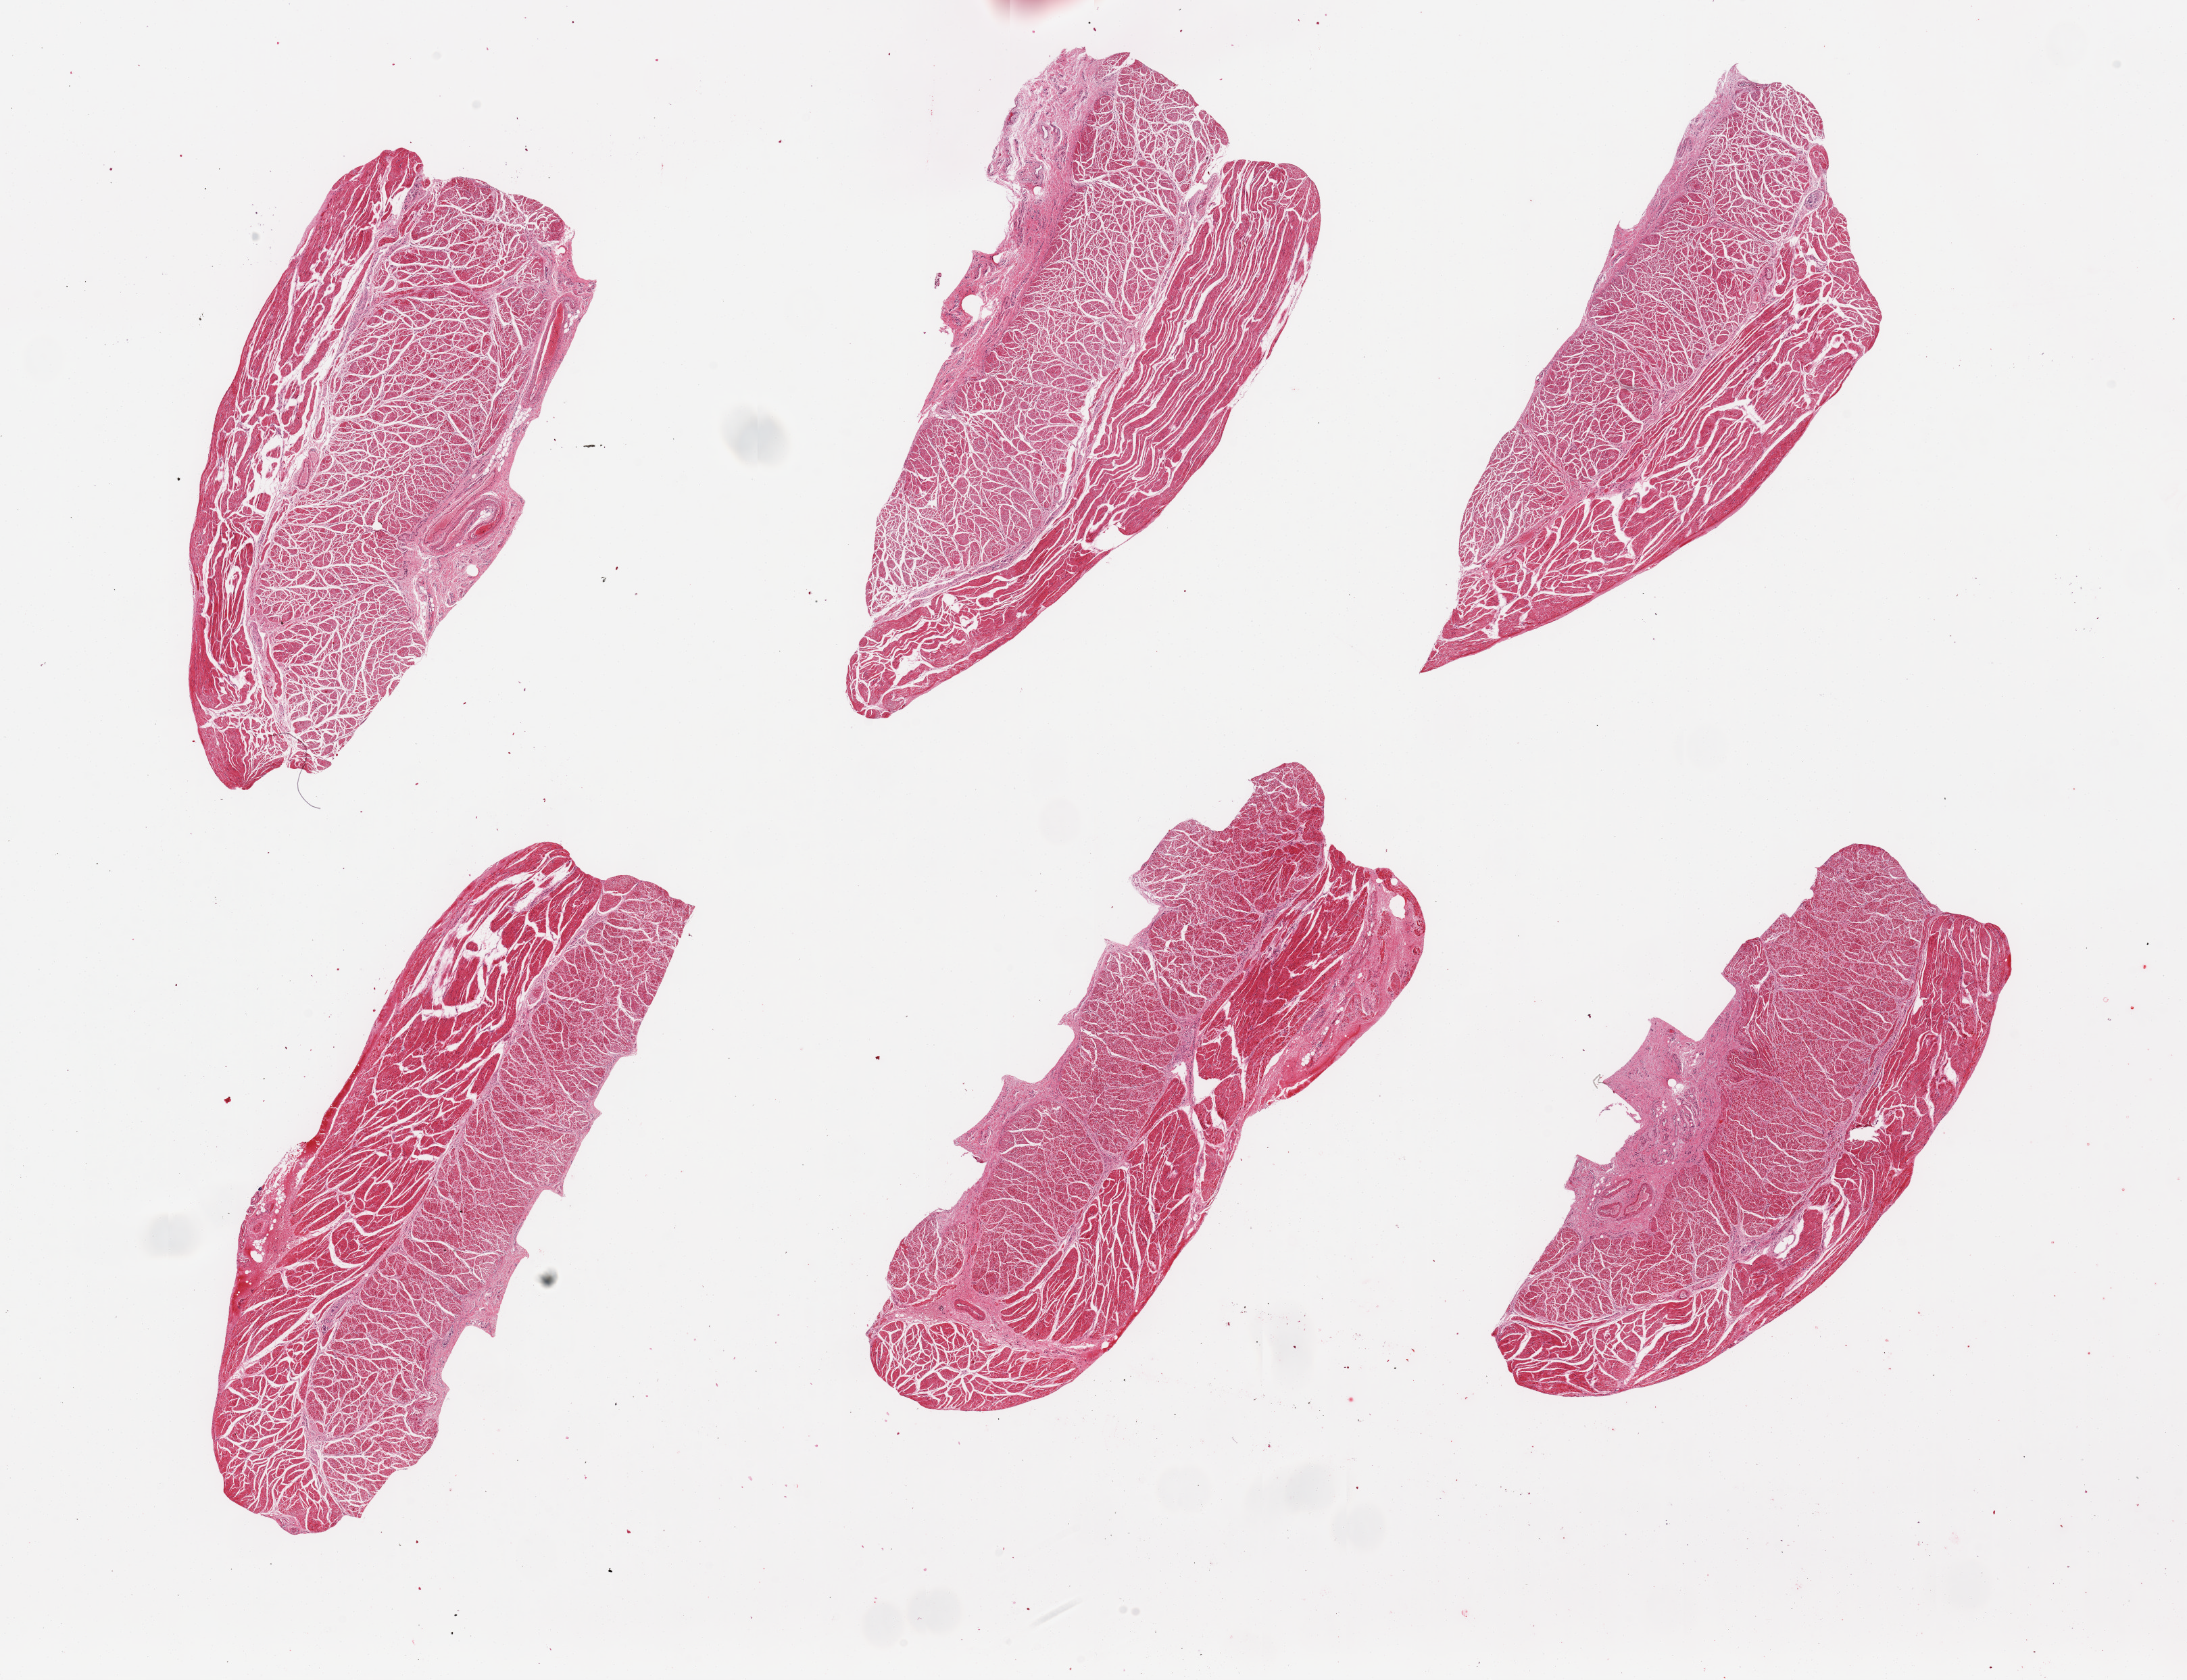
Whole-slide image, hematoxylin and eosin (H&E) stain — a low-resolution overview of the entire scanned area, about 25.6 x 19.7 mm; PAXgene-fixed, paraffin-embedded tissue; section of esophageal muscle (target tissue); donor tissue sample. Donor: male.
Reviewer comment on this tissue sample: 6 pieces; muscularis.